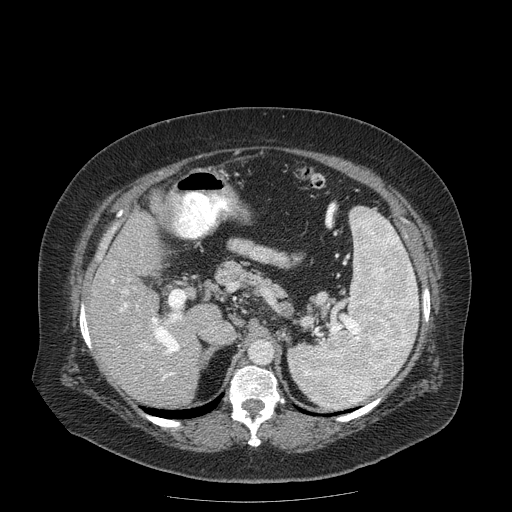
Contrast-enhanced abdominal CT (liver protocol), one axial slice; position 105 of 204 along the scan axis; 120 kVp; soft-tissue window (W 400 / L 40 HU); 2.5 mm slice thickness; 512 × 512 image matrix. Case-level facts recorded for this patient, not image findings: diagnosis: hepatocellular carcinoma (patient treated with transarterial chemoembolisation; whether this scan precedes or follows treatment is not stated here); TNM stage (as recorded): Stage-IIIB; Child-Pugh class: A; tumour nodularity: uninodular.
Annotated regions visible in this slice (semi-automatically segmented with operator editing):
- liver parenchyma outside the tumour (the mass and vessels are separate outlines, so this box may not span the whole liver): bounding box <90,196,202,406> (left, top, right, bottom; pixels)
- liver vessels: <112,280,182,380>